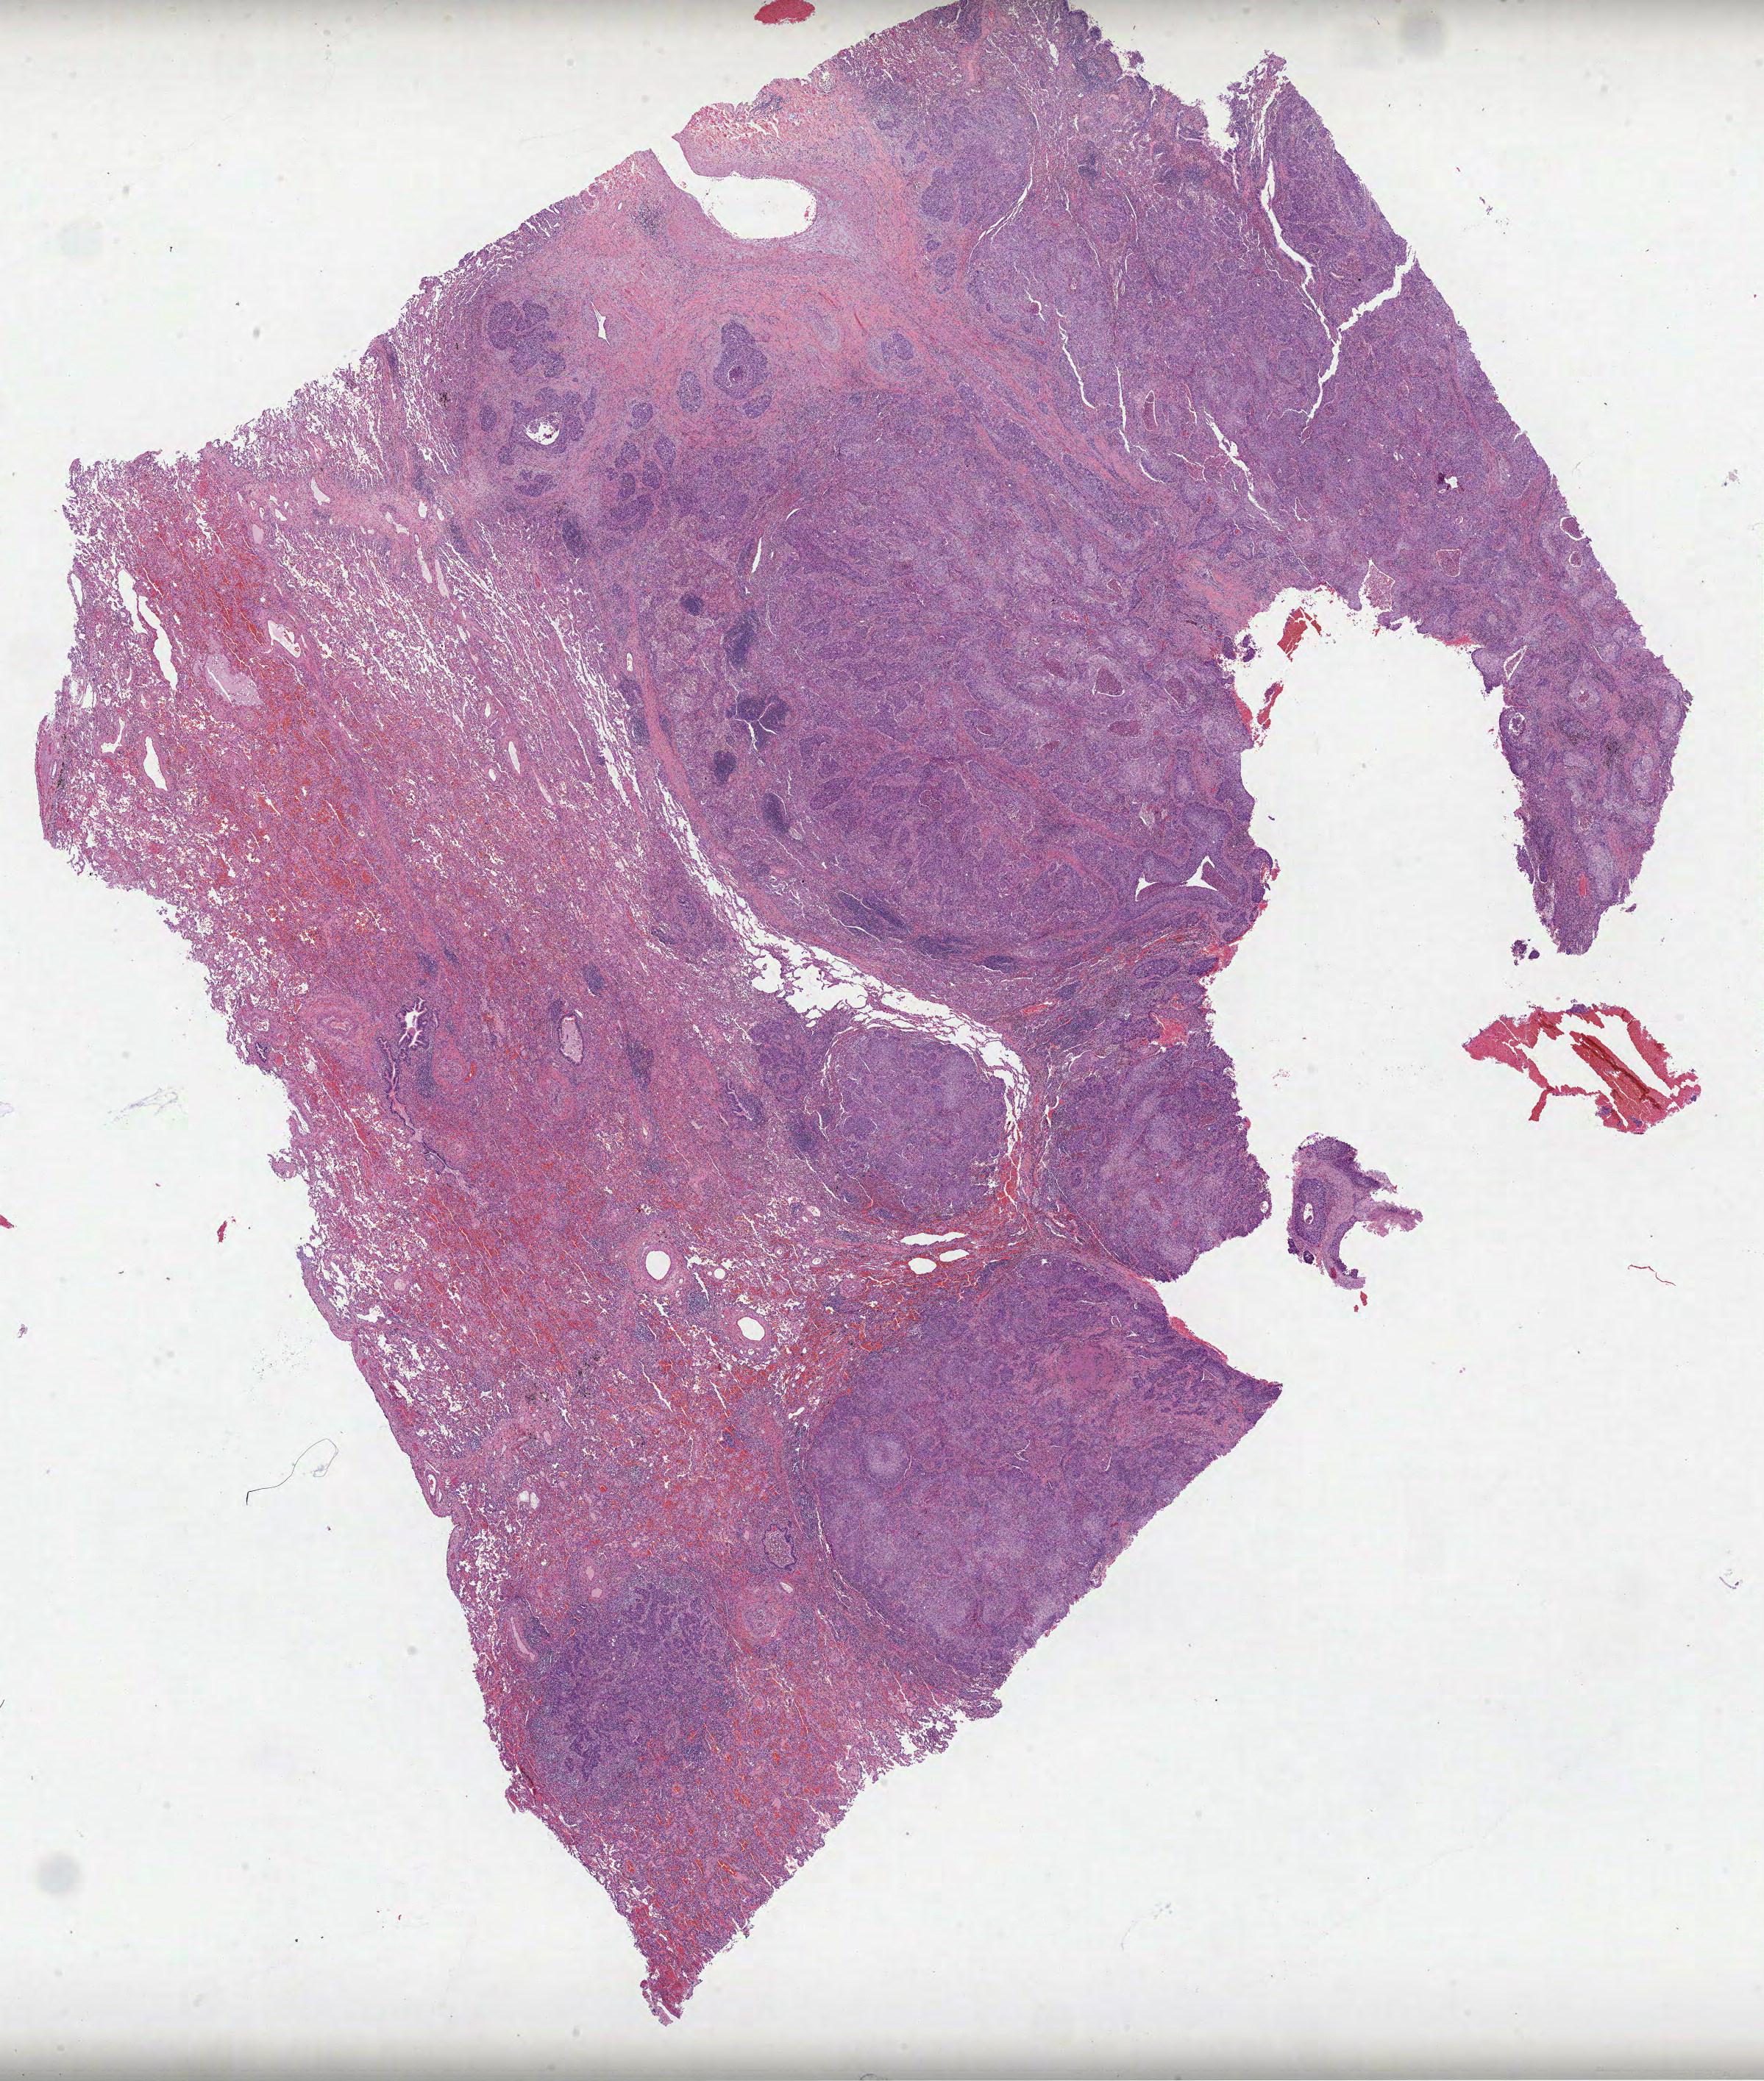
Whole-slide histology image, H&E, a low-resolution overview of the entire scanned area, about 19.3 x 22.8 mm (acquisition: 40x scan), formalin-fixed paraffin-embedded (FFPE) diagnostic section, sample: primary tumour, lung. Male patient; age at initial diagnosis 55 years.
Diagnosis: Squamous cell carcinoma, NOS. AJCC pathologic stage: IIA (7th edition). TNM: T2a N1 M0.